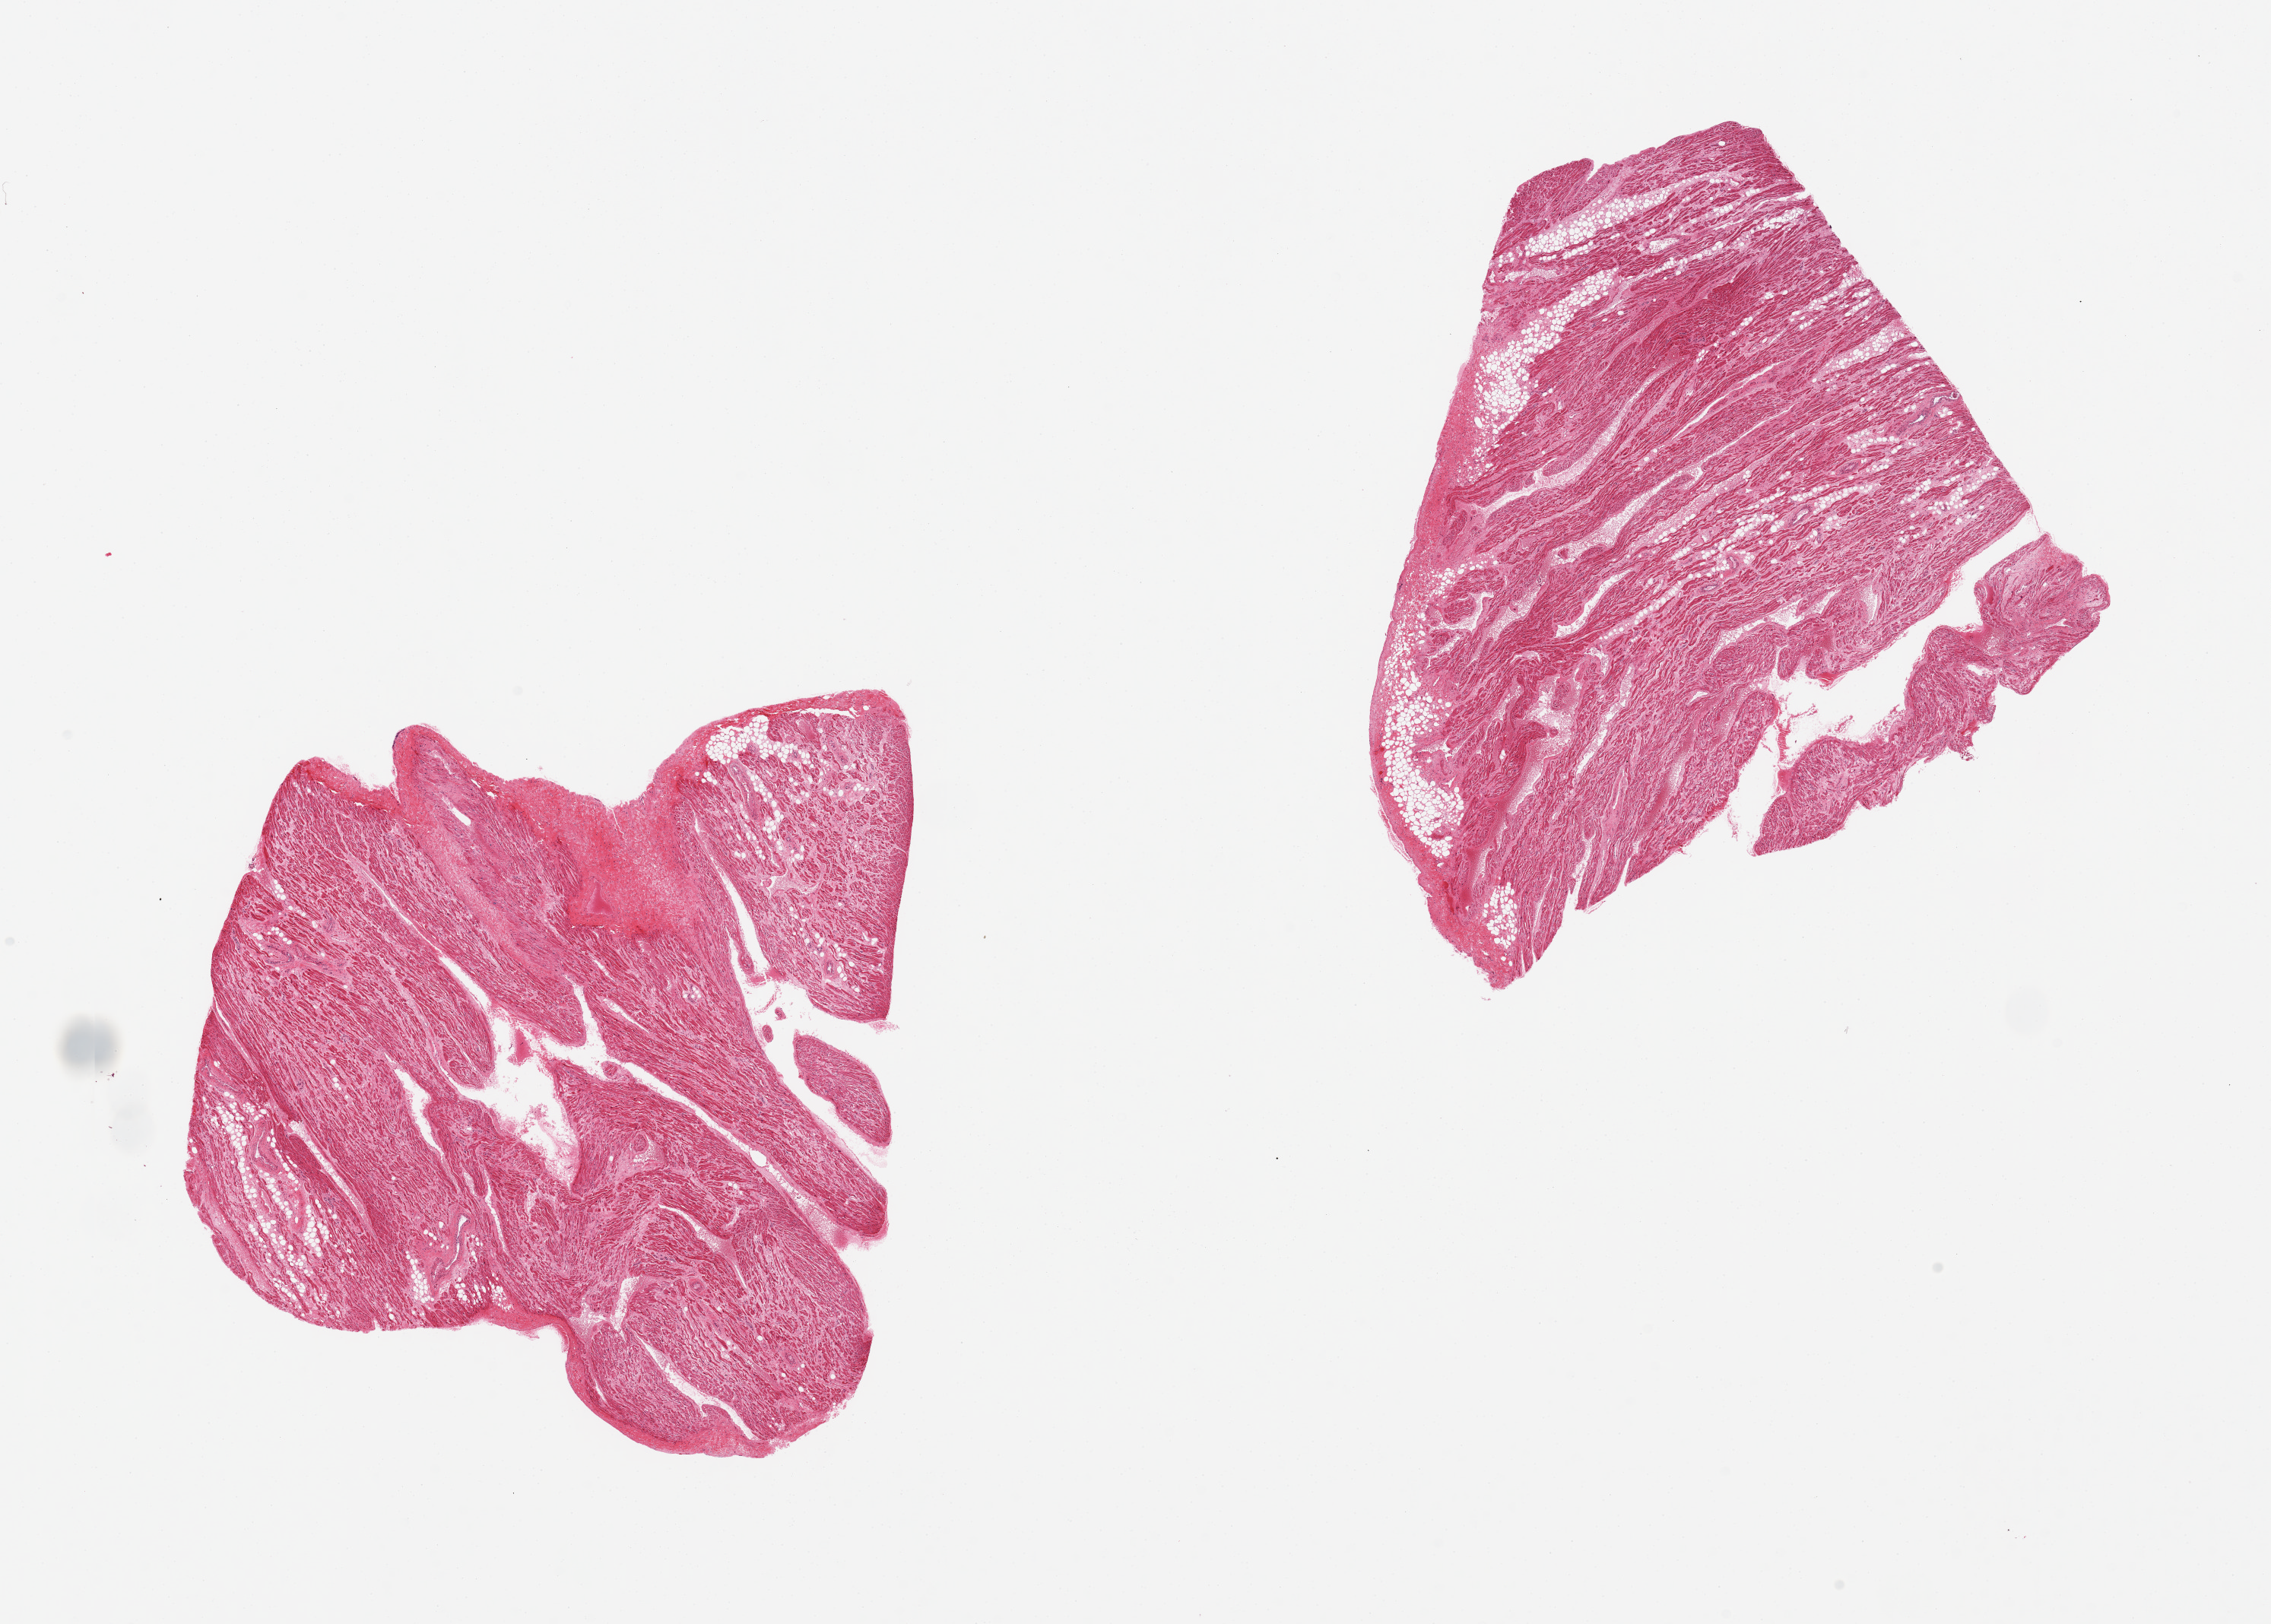
H&E whole-slide image — whole scanned area (about 23.6 x 16.9 mm) shown as a low-resolution overview. PAXgene-fixed paraffin-embedded (PFPE) section. Target tissue: auricular appendage. Donor tissue sample. Donor sex: male.
* pathologist's review note for this sample: 2 pieces, includes up to ~10% internal adipose tissue